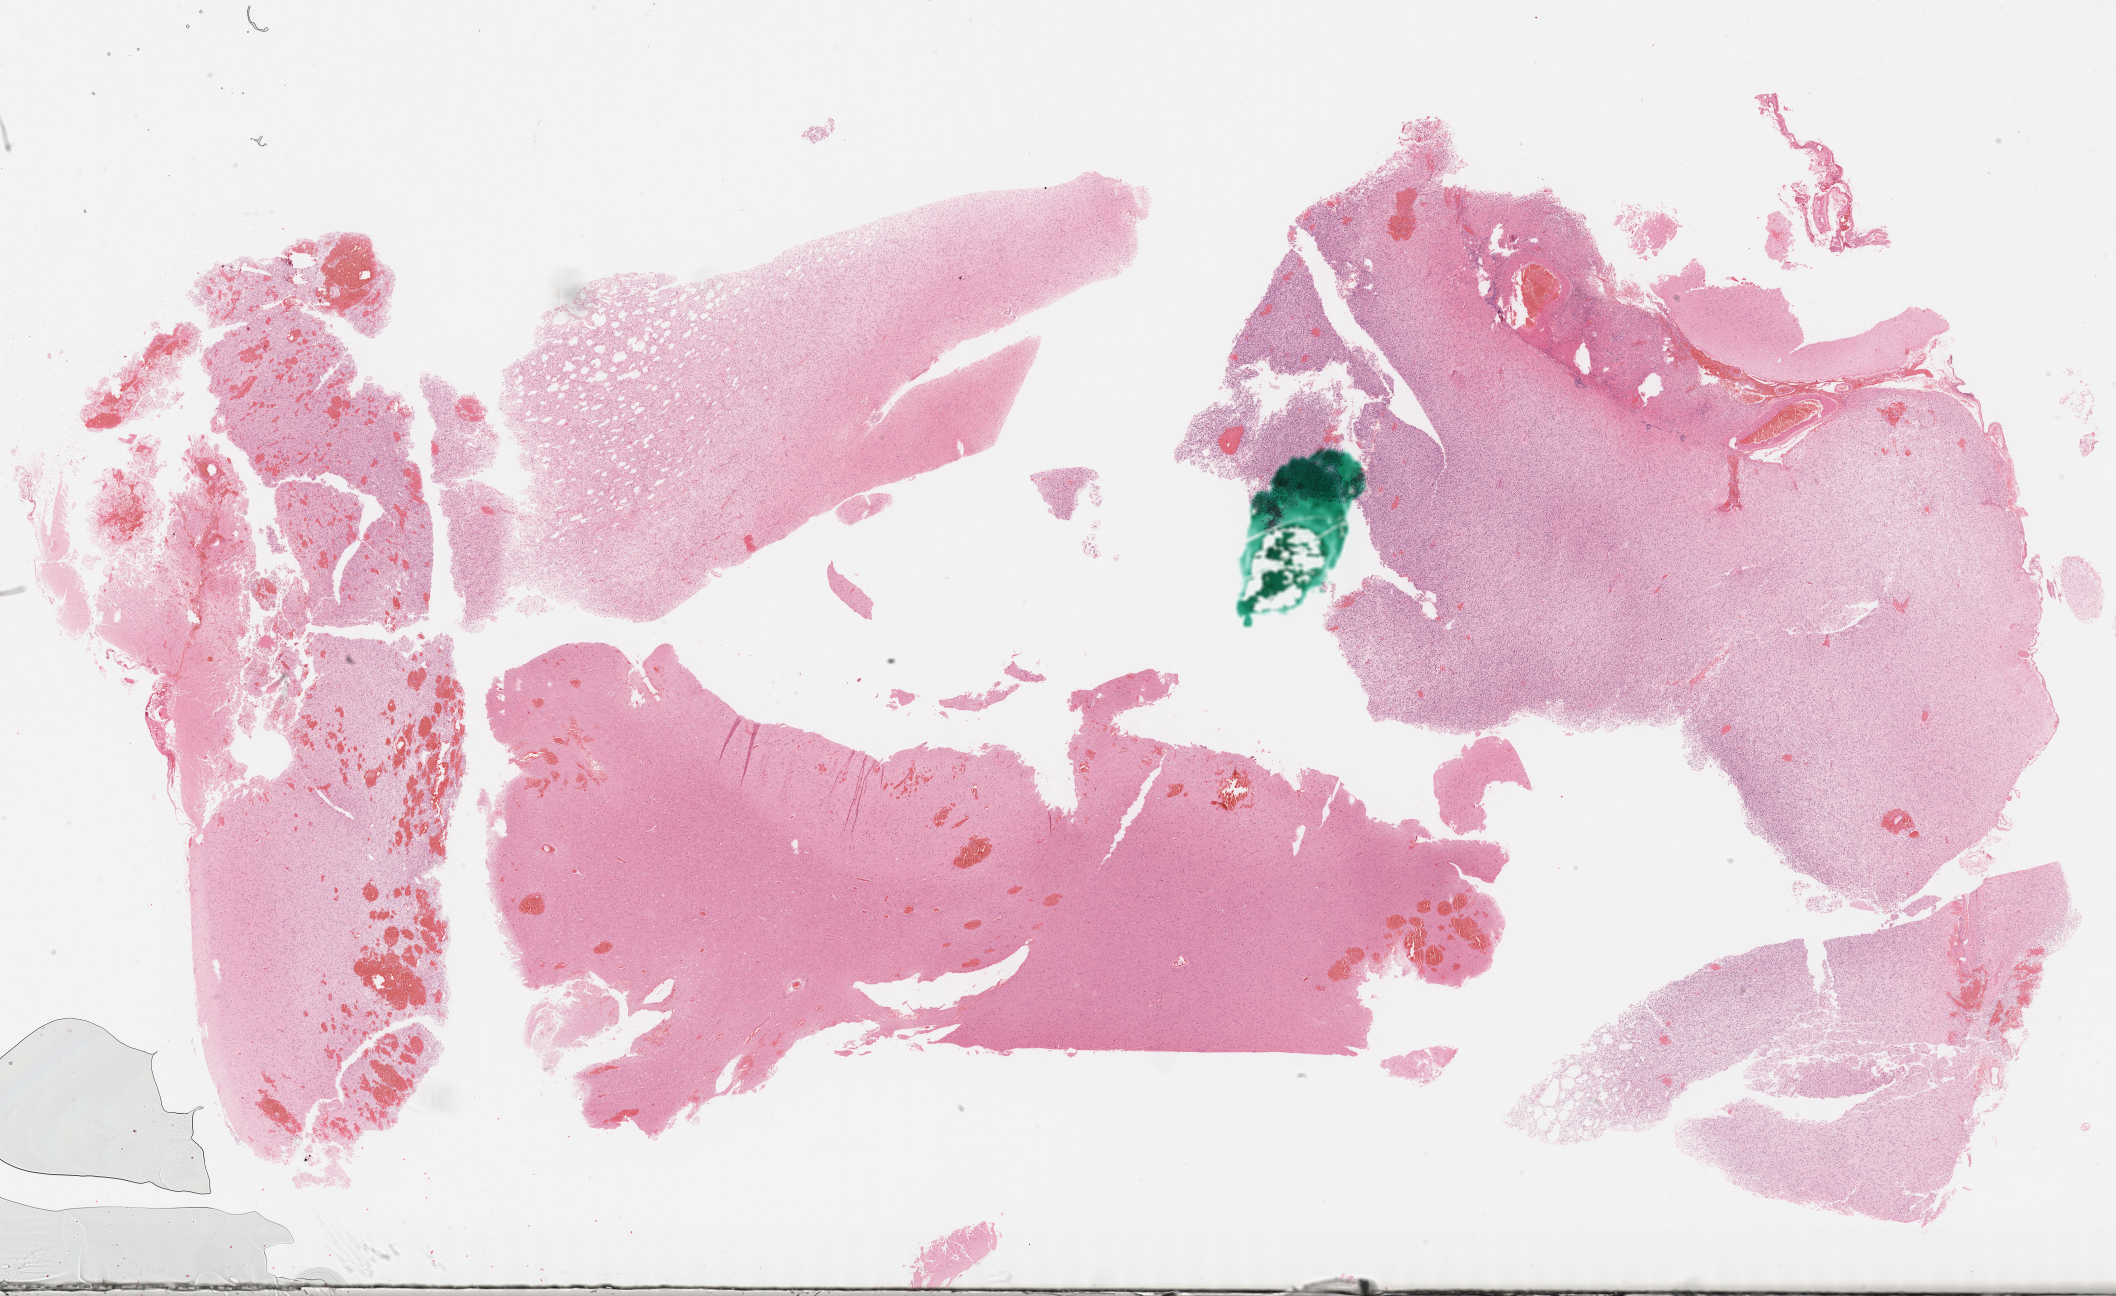
Whole-slide histology image, H&E-stained, shown as a low-resolution overview of the whole scanned area (about 34.2 x 21.0 mm, from a 40x scan), formalin-fixed paraffin-embedded (FFPE) diagnostic section, primary tumour sample from the brain. Male, age 36 years at initial diagnosis.
Histologic diagnosis: Astrocytoma, anaplastic (cerebrum).